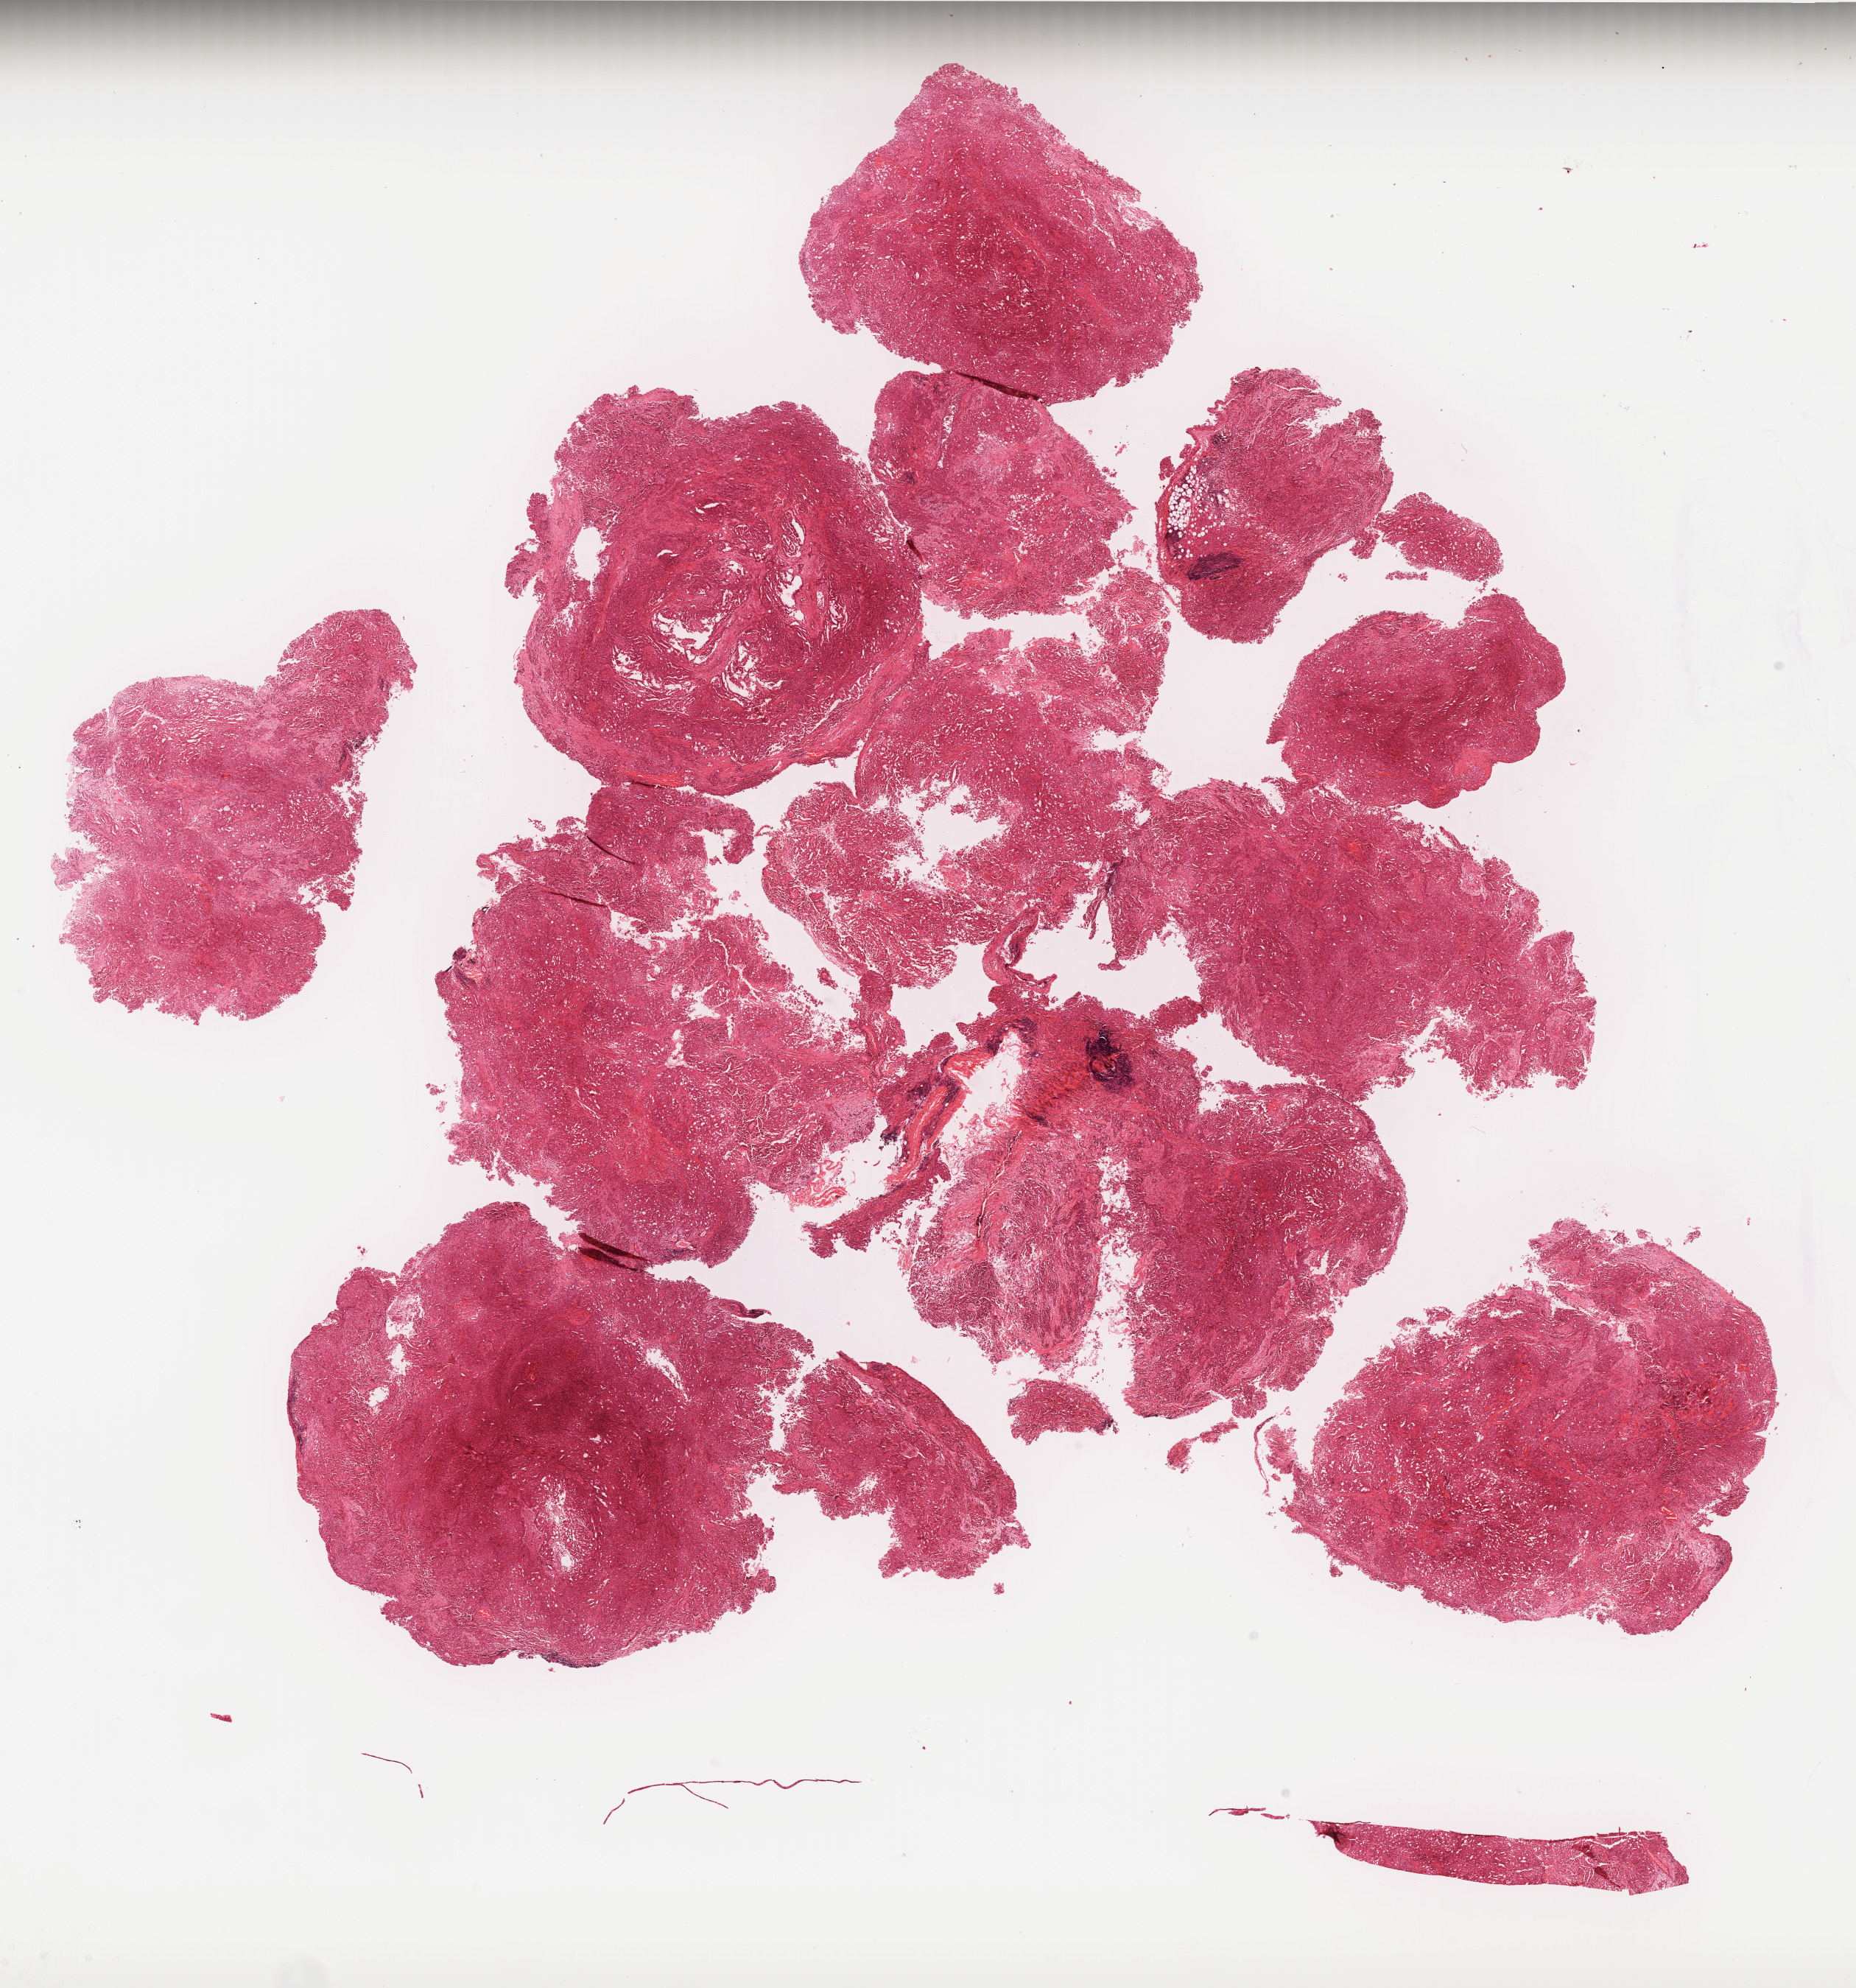
H&E-stained whole-slide image, whole scanned area (about 20.2 x 21.6 mm) shown as a low-resolution overview. FFPE section. Primary tumour sample from the mesothelium. Male, age 68 years at initial diagnosis.
• AJCC pathologic stage: IV (7th edition)
• laterality: right
• TNM: T2 N0 M1
• diagnosis: Epithelioid mesothelioma, malignant (pleura, NOS)